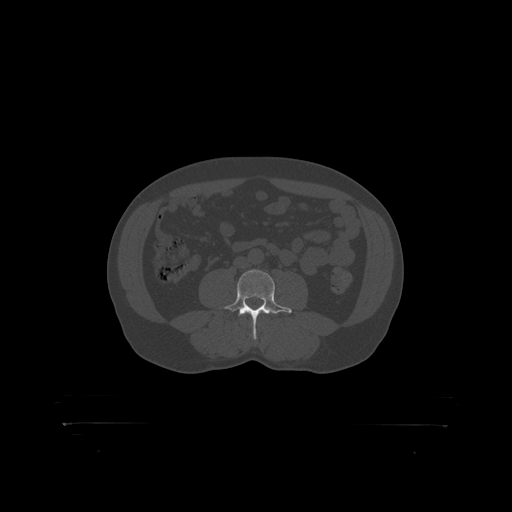
CT including the spine, one axial slice. Slice 240 of 399 in the series (ordered by position). Reconstruction kernel STANDARD. 120 kVp. Bone window (W 1800 / L 400 HU). 1.25 mm slice thickness. 512 × 512 image matrix. Patient: male, 46 years. From the clinical record (not read from this slice): primary cancer: skin.
Annotated regions visible in this slice (semi-automatic segmentation, software-assisted and operator-edited):
- L4 vertebra: bounding box (x1, y1, x2, y2) in pixels: (221, 270, 290, 319)